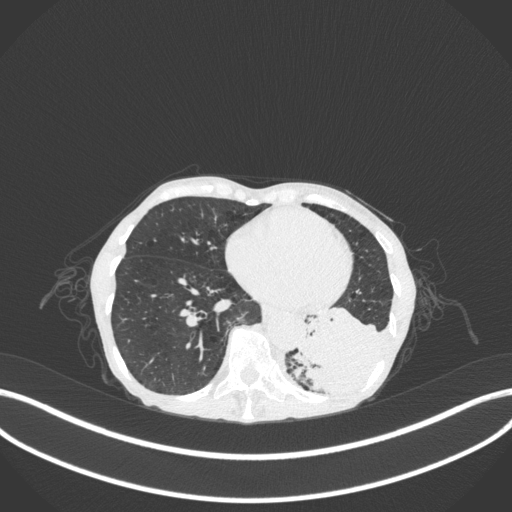
Chest CT, one axial slice; reconstruction kernel B31f; 120 kVp; lung window (W 1500 / L -600 HU); 1 mm slice thickness; 512 × 512 image matrix, field of view 400 × 400 mm. Female patient, age 70 years. From the clinical record (not read from this slice): clinical TNM (as recorded): T3 N0 M0; histopathological grade: G3.
Structures marked on this image (bounding box drawn by a radiologist):
- lung tumour (recorded histology: small cell carcinoma): bounding box [x1, y1, x2, y2] px = [292, 300, 400, 402]